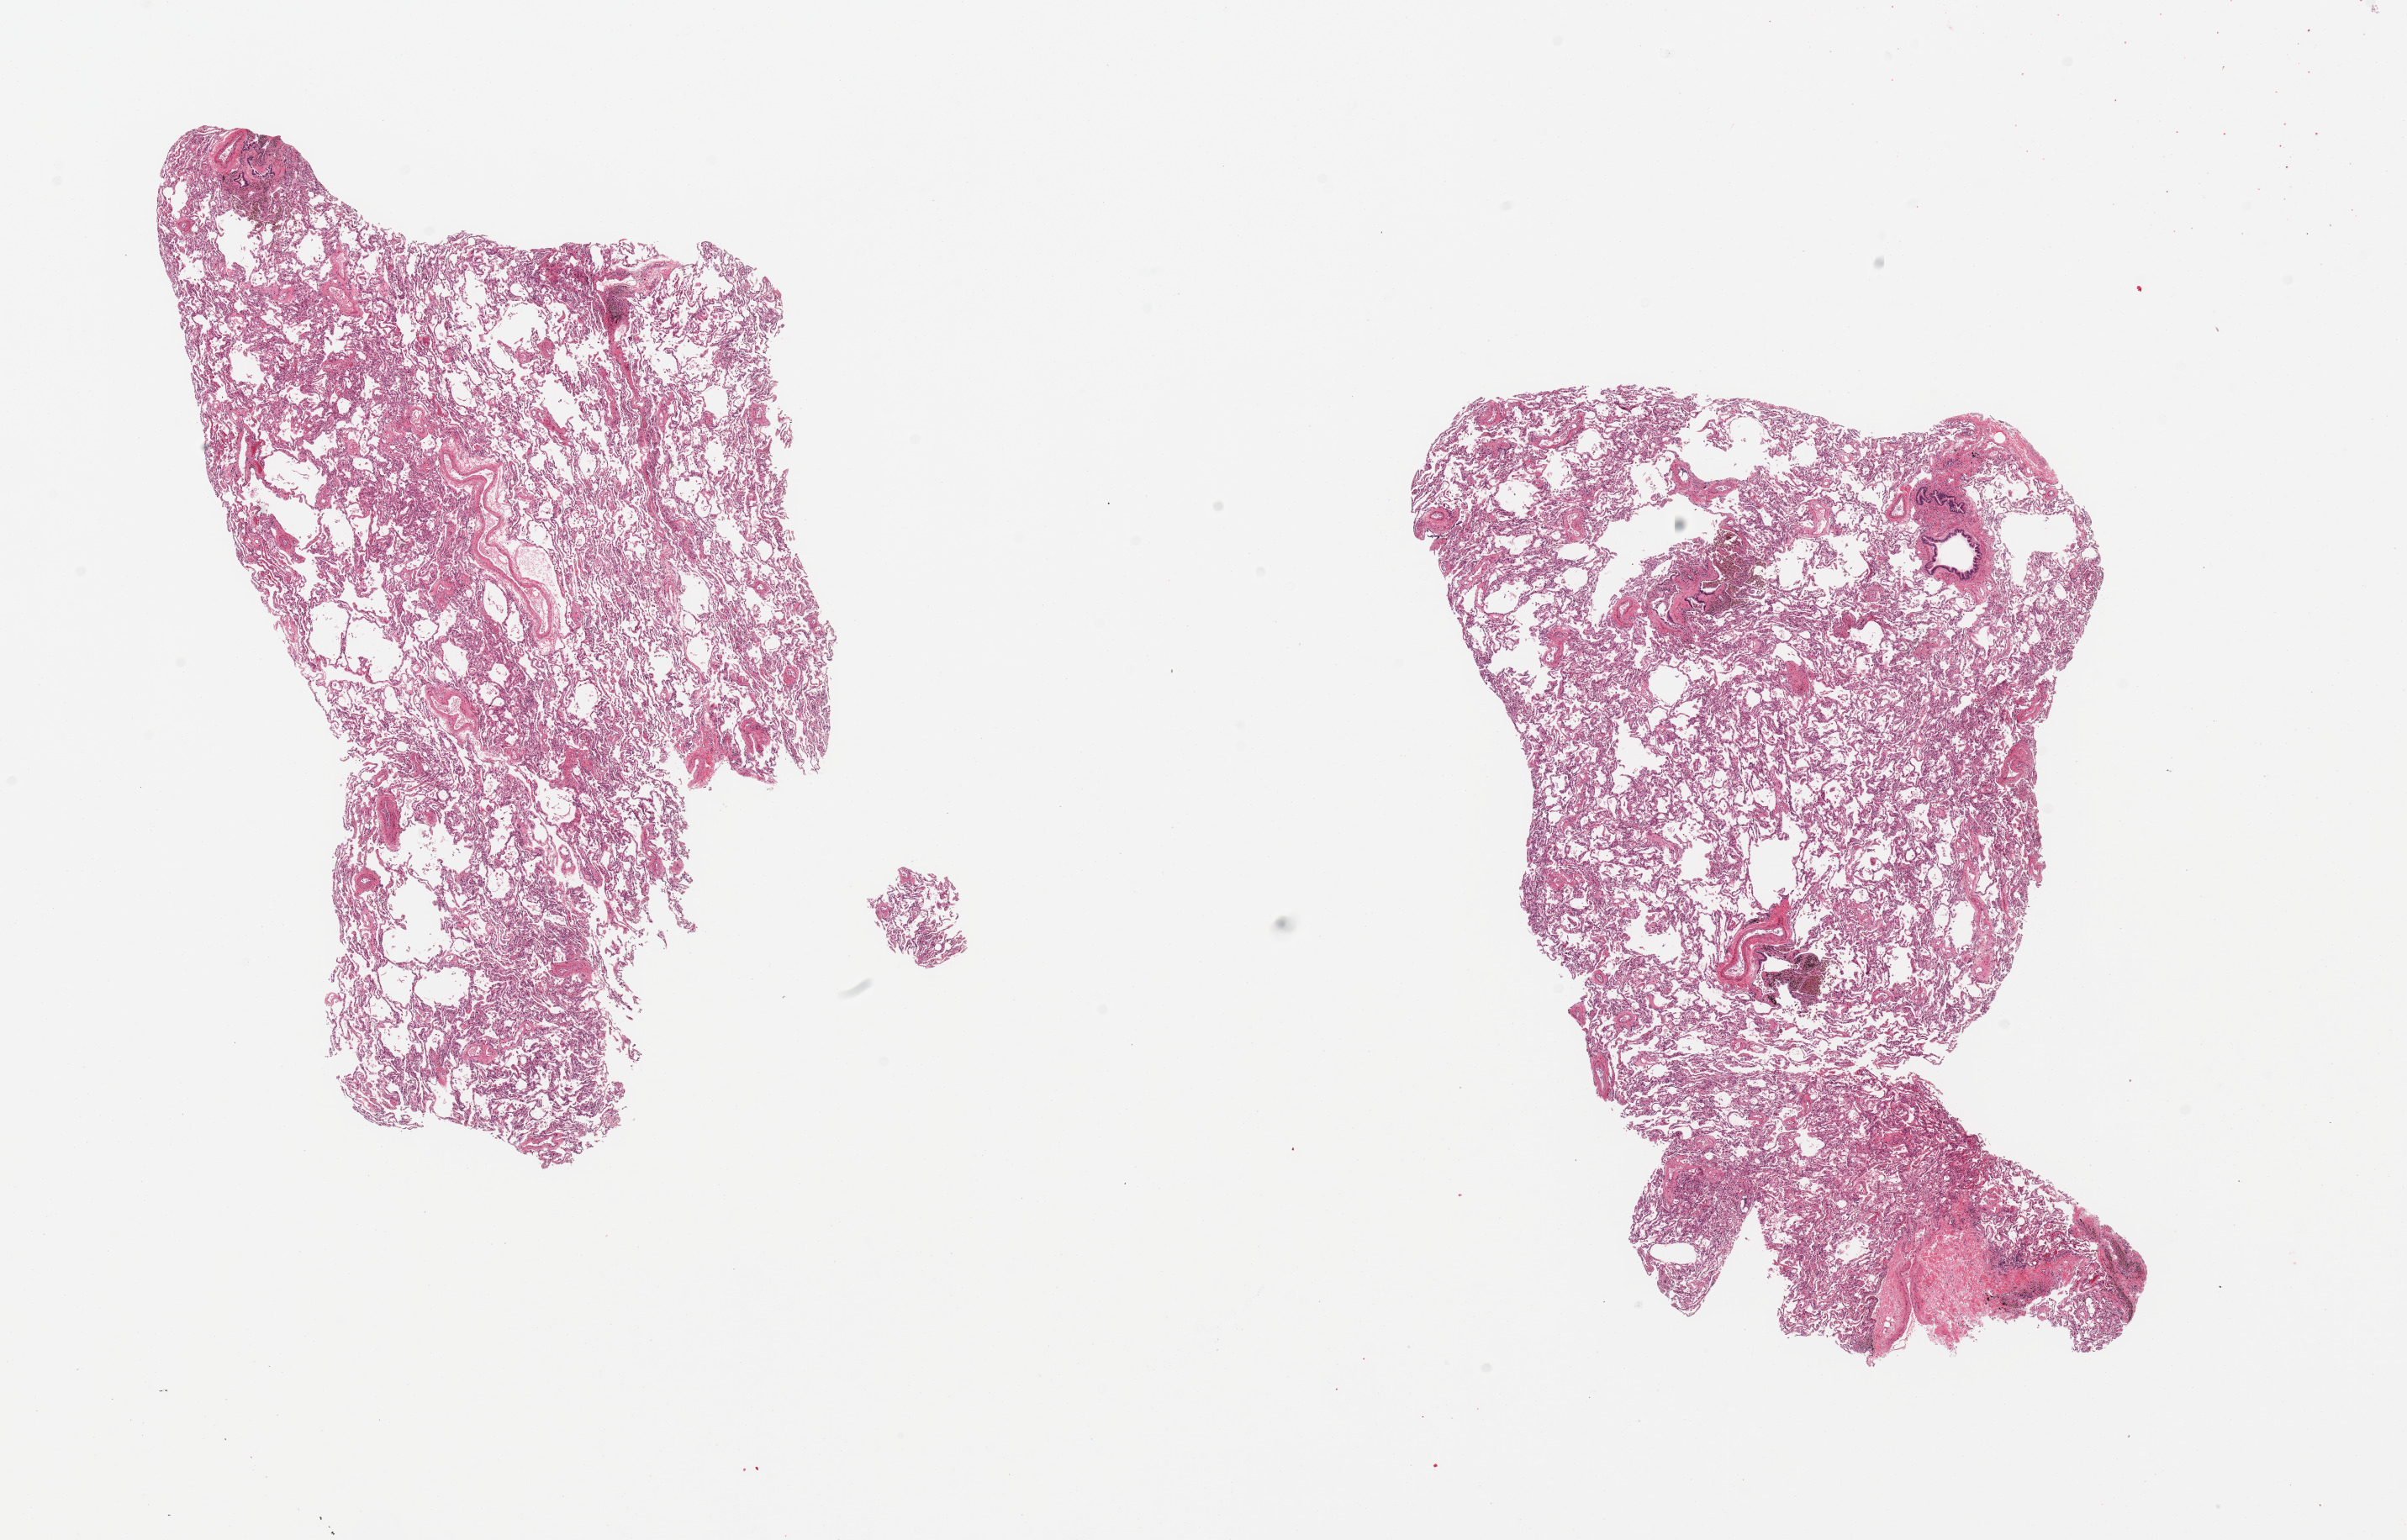
Whole-slide image, haematoxylin and eosin stain — a low-resolution overview of the entire scanned area, about 22.6 x 14.5 mm, PAXgene-fixed paraffin-embedded (PFPE) section, section of lung (target tissue), donor tissue sample.
Pathologist's review note for this sample: 2 pieces; foci of pigmented macrophages.